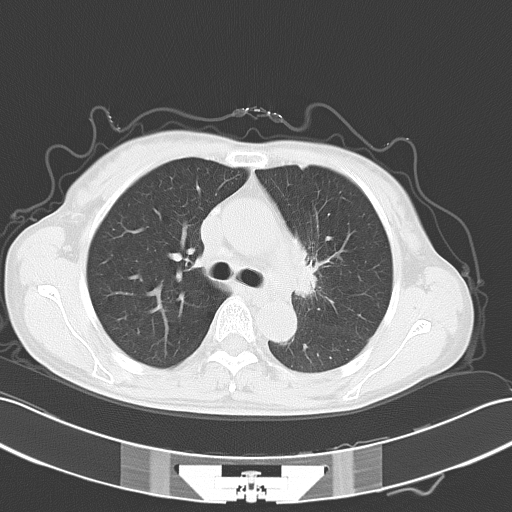
Chest CT, one axial slice. Slice 37 of 54 in the series (ordered by position). Reconstruction kernel B70f. 120 kVp. Lung window (W 1500 / L -600 HU). 5 mm slice thickness. 512 × 512 image matrix, field of view 353 × 353 mm. Patient: female, 50 years. From the clinical record (not read from this slice): clinical TNM (as recorded): T2a N1 M1c.
Annotated regions visible in this slice (bounding box drawn by a radiologist):
- lung tumour (recorded histology: adenocarcinoma): bounding box (x1, y1, x2, y2) in pixels: (292, 230, 323, 303)